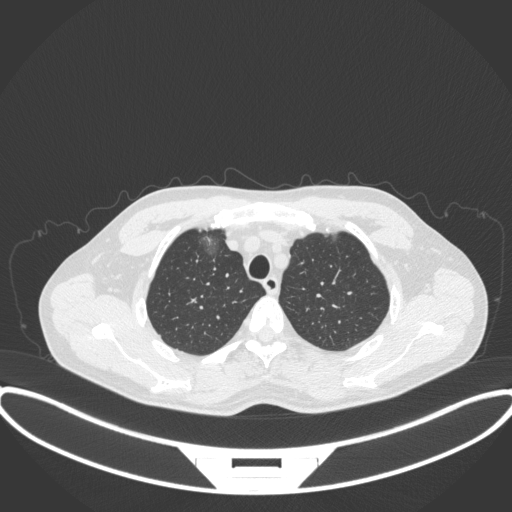
Chest CT, one axial slice. Slice 301 of 395 in the series (ordered by position). 120 kVp. Lung window (W 1500 / L -600 HU). 512 × 512 image matrix, field of view 424 × 424 mm. Male patient, age 60 years. From the clinical record (not read from this slice): clinical TNM (as recorded): T1c N0 M0.
Outlined on this slice (bounding box drawn by a radiologist):
- lung tumour (recorded histology: adenocarcinoma): box from (x=200, y=232) to (x=225, y=259) px